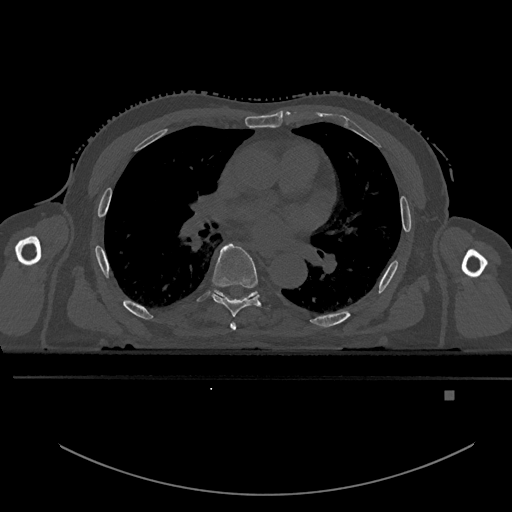
CT including the spine, one axial slice; position 300 of 969 along the scan axis; bone window (W 1800 / L 400 HU); 512 × 512 image matrix, field of view 456 × 456 mm. Male patient, age 82 years. From the clinical record (not read from this slice): primary cancer: prostate; vertebrae with lytic lesions (as recorded): T11, T9, T8, T2.
Structures marked on this image (semi-automatically segmented with operator editing):
- T5 vertebra: bounding box (x1, y1, x2, y2) in pixels: (230, 322, 236, 330)
- T6 vertebra: (212, 243, 261, 317)
- T7 vertebra: (217, 292, 256, 298)